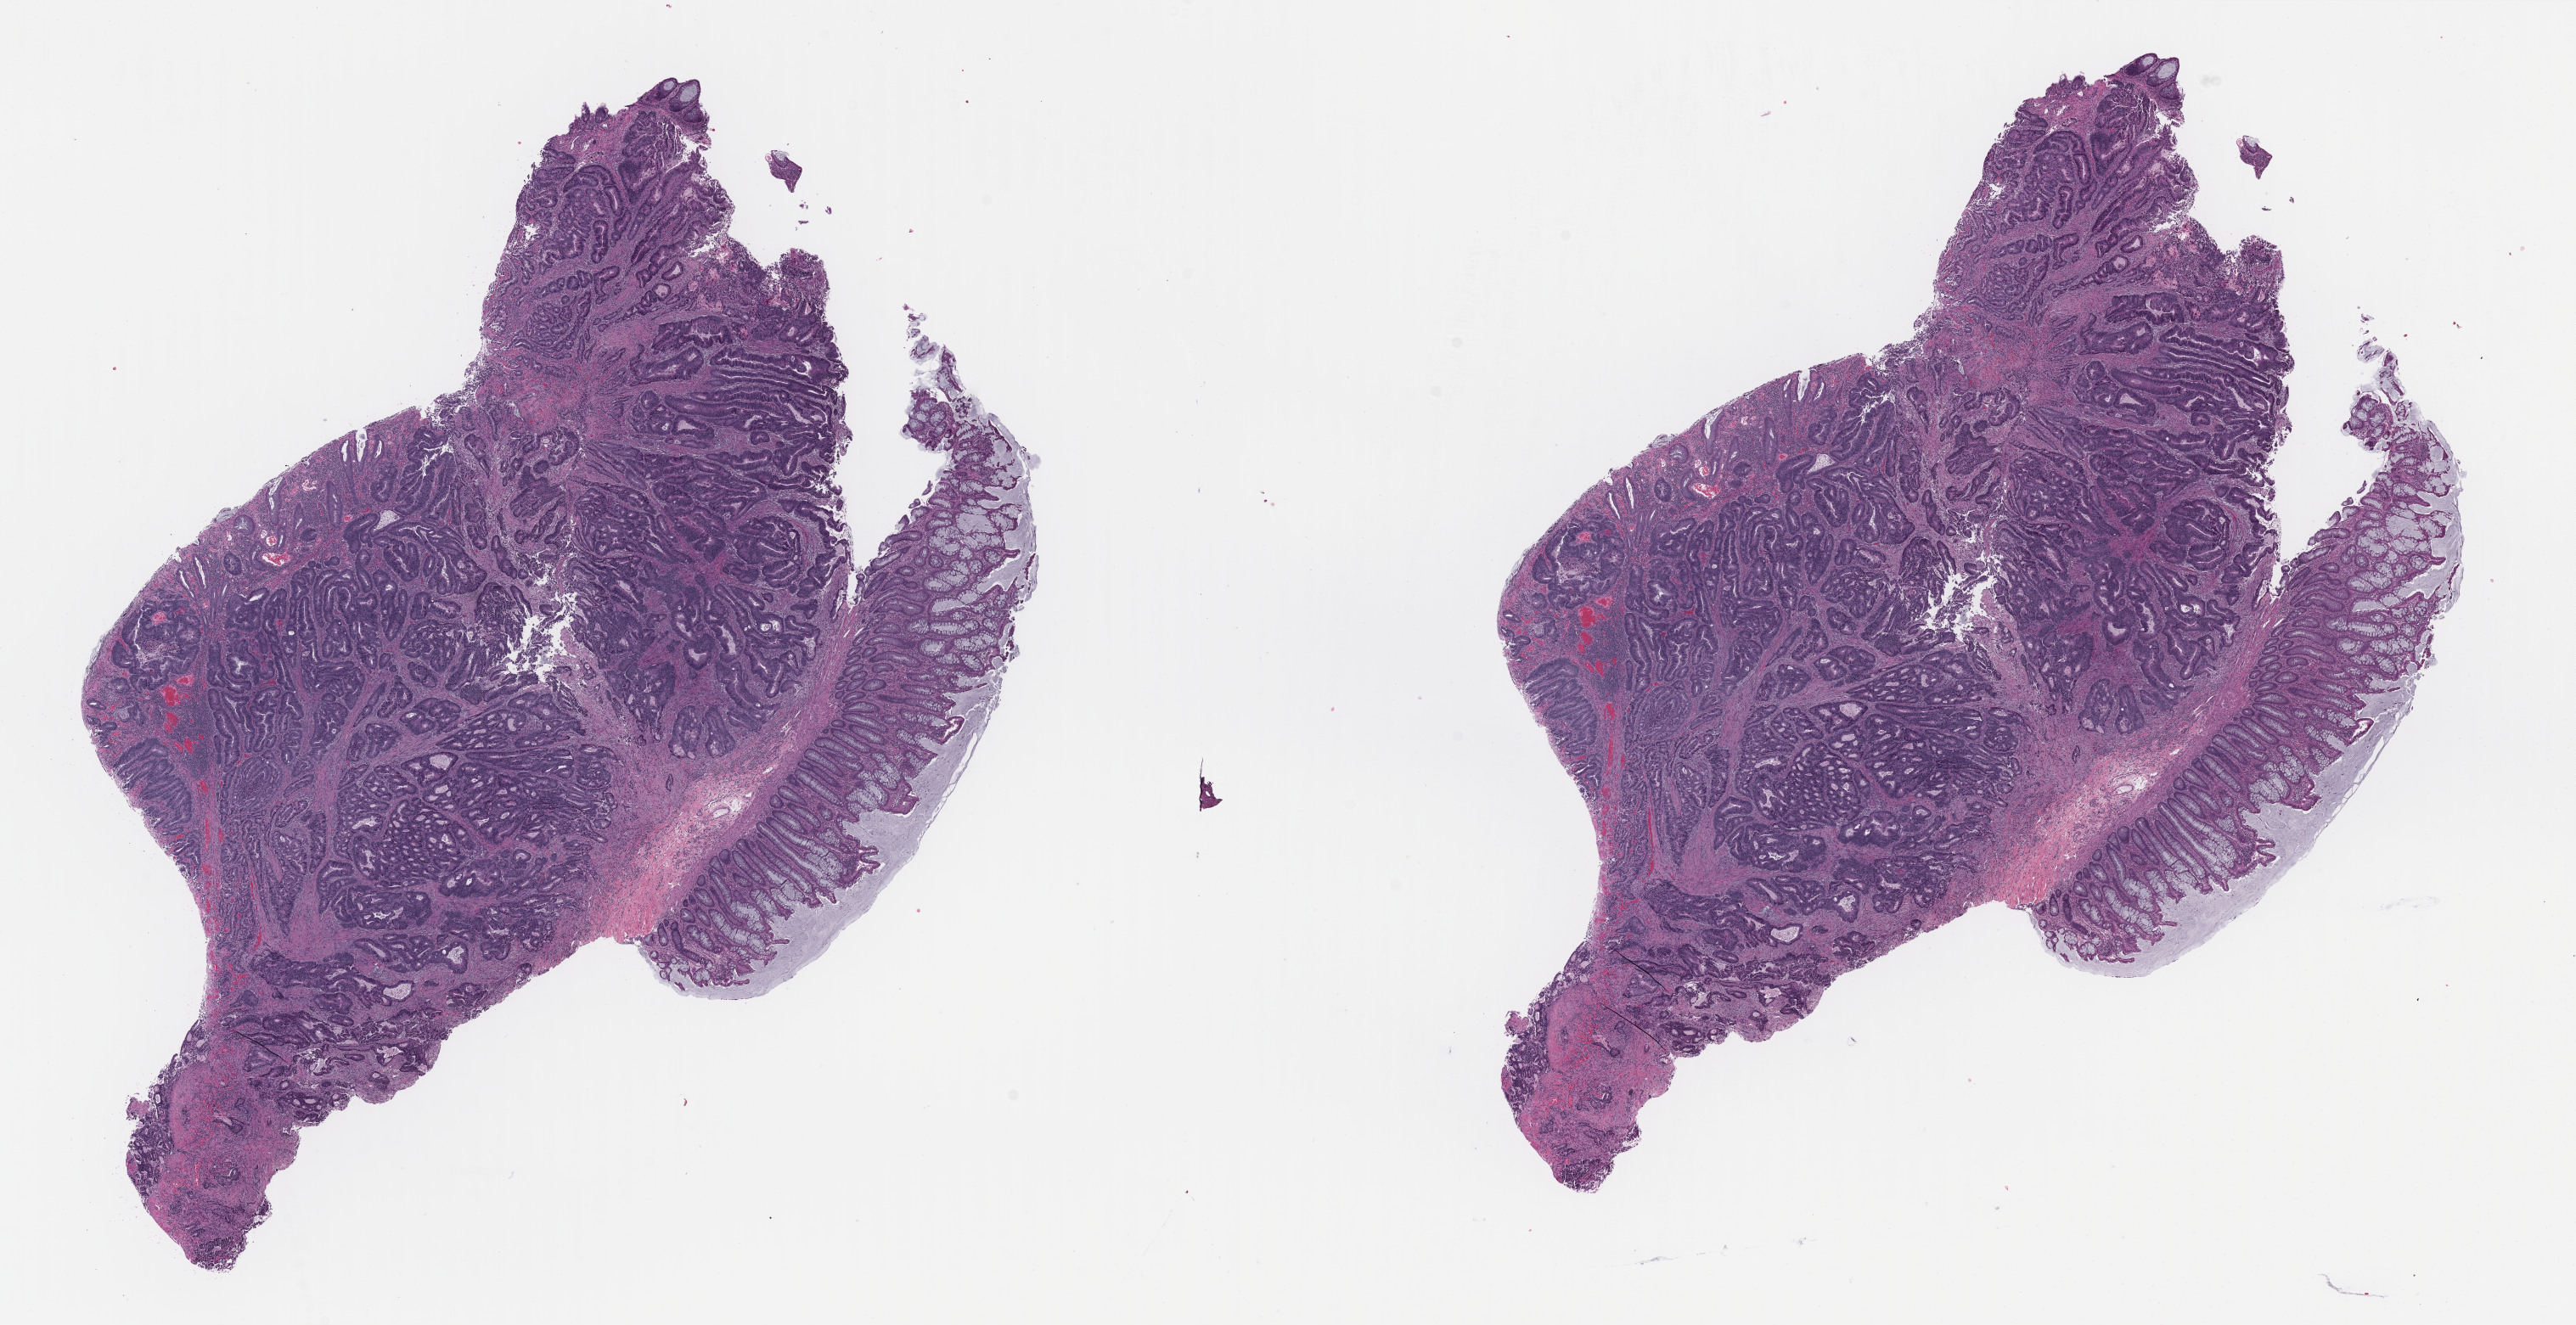
Whole-slide histology image, Hematoxylin and eosin (H&E) stained, a low-resolution overview of the entire scanned area, about 24.0 x 12.4 mm (from a 40x scan). Formalin-fixed paraffin-embedded (FFPE) diagnostic section. Sample: primary tumour, colon. Male patient; age at initial diagnosis 44 years.
AJCC pathologic stage: IVA (7th edition). Pathologic diagnosis: Adenocarcinoma, NOS (sigmoid colon).